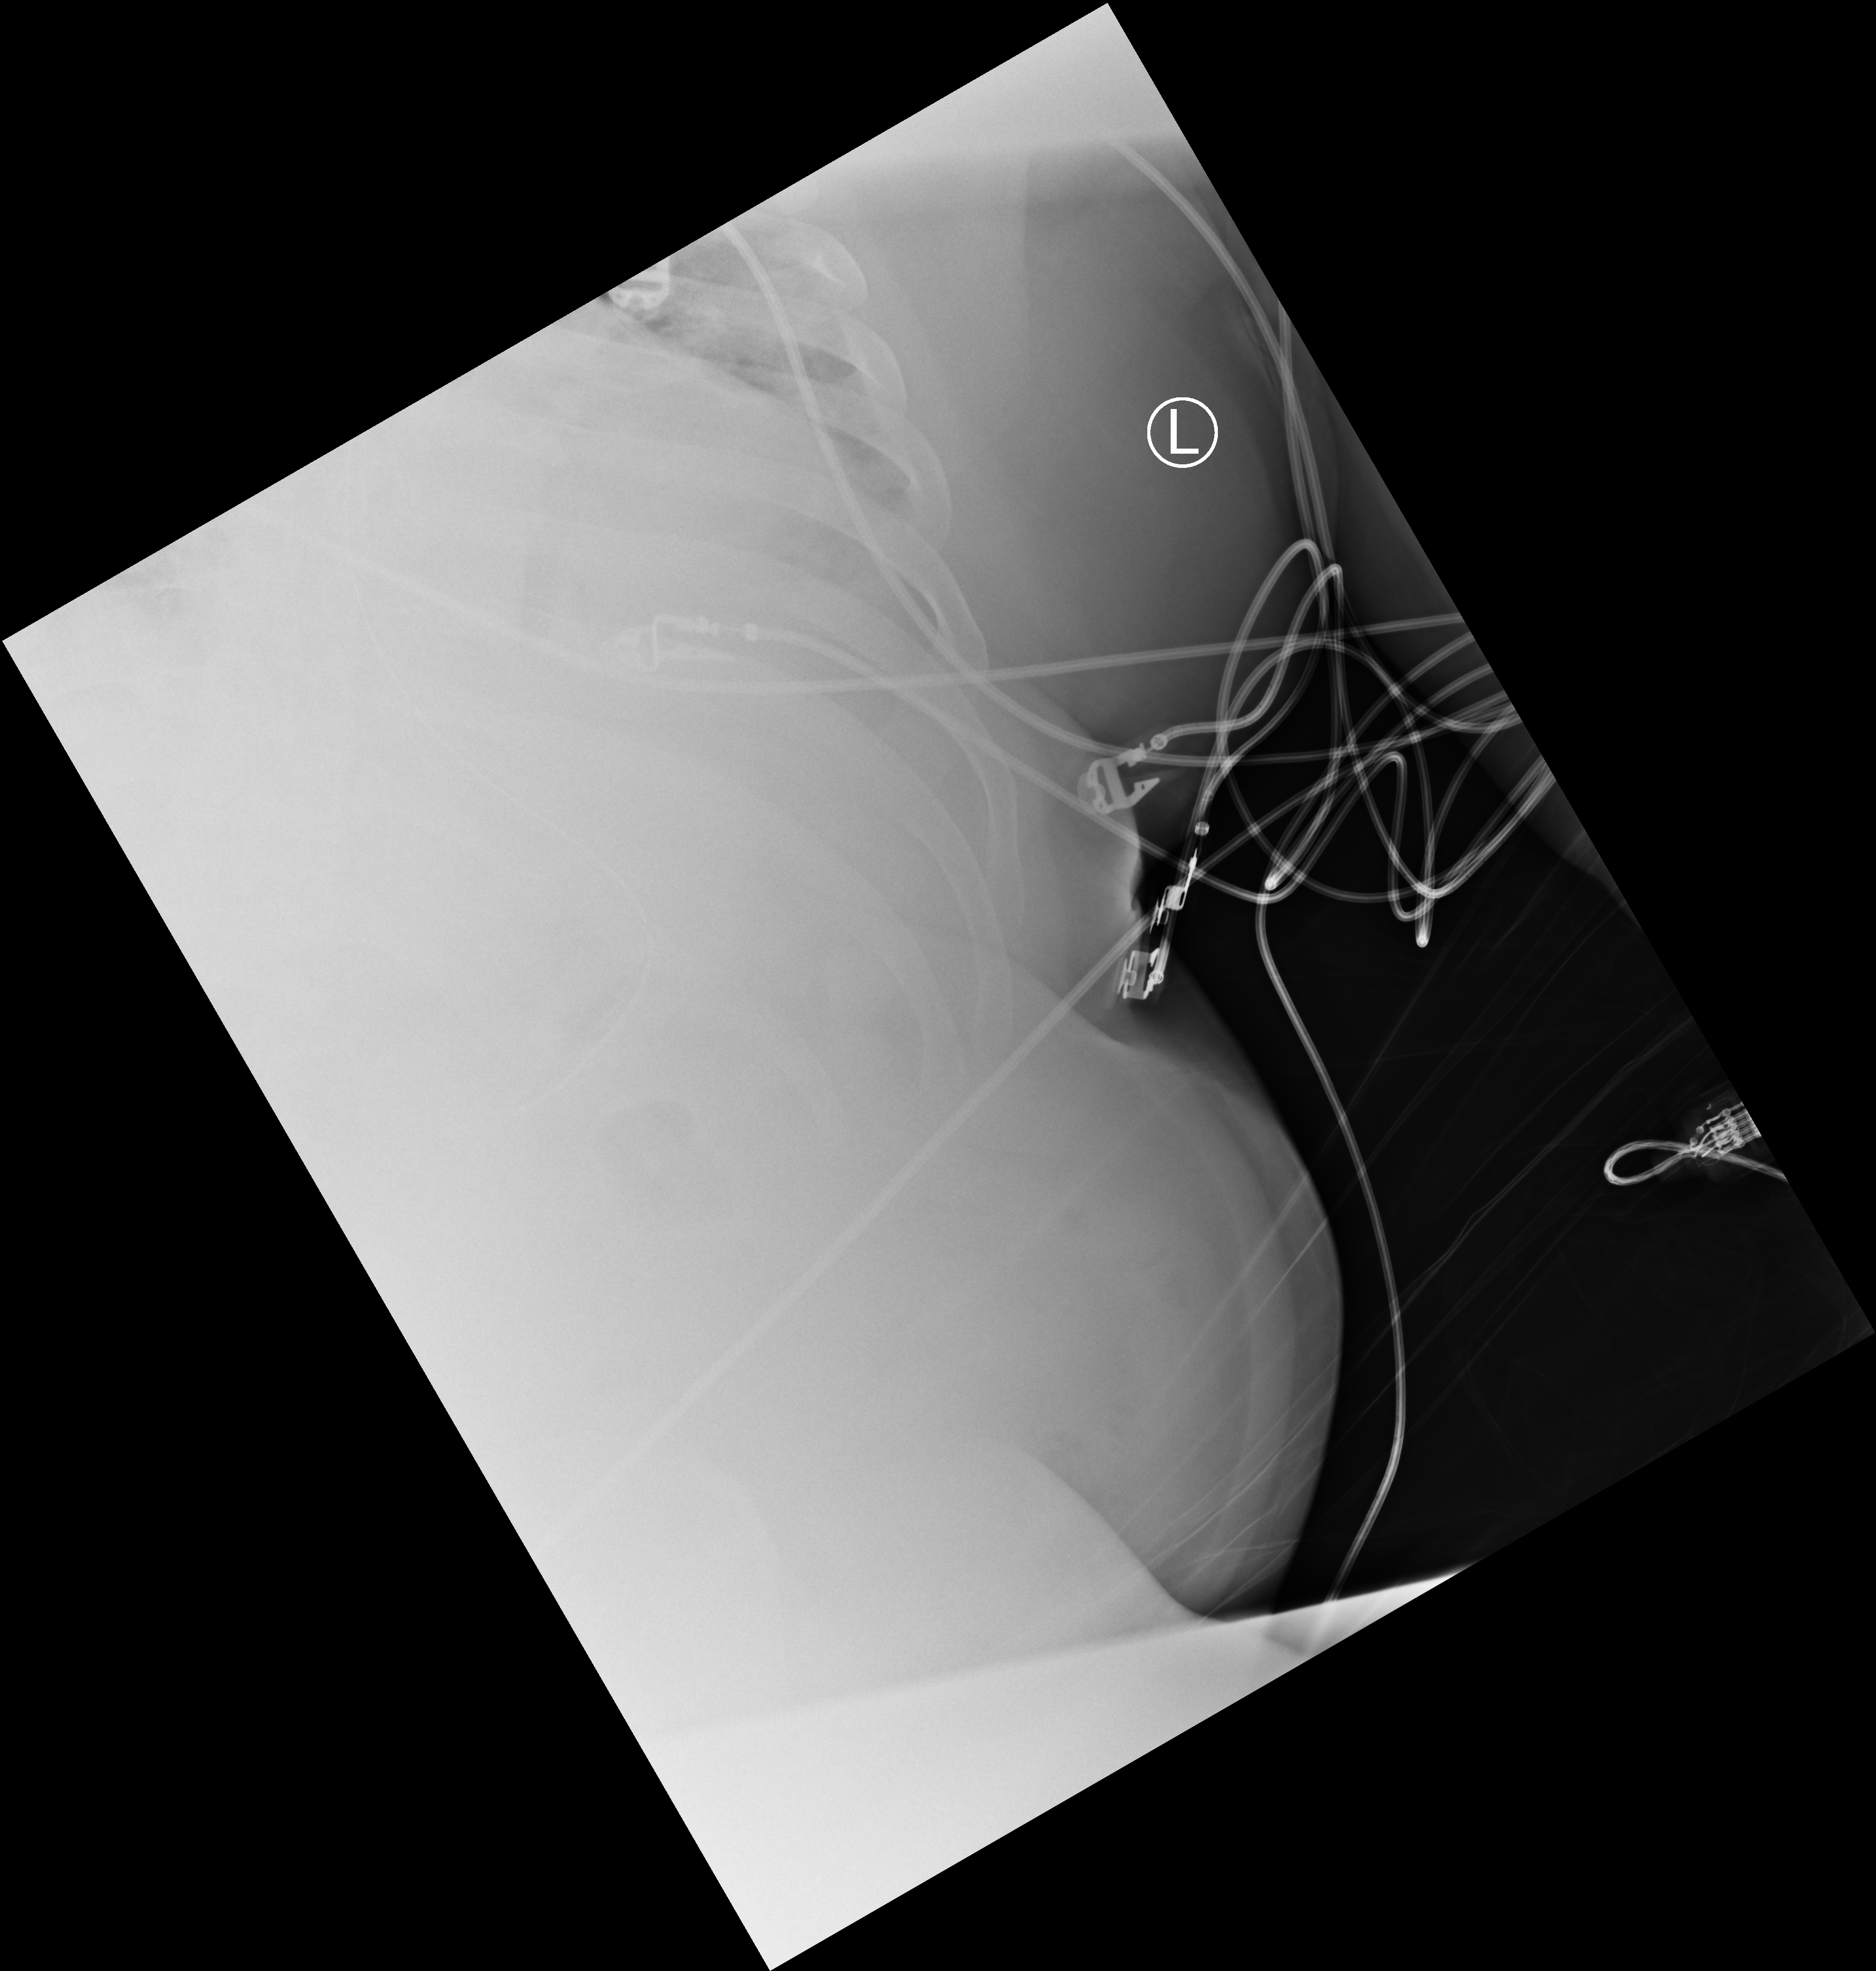
Chest X-ray (portable); anteroposterior (AP) projection. Patient hospitalised with COVID-19; male, aged 18–59 years.
Hospital-stay facts (about this admission, not read from this image; timing relative to this image not recorded): mechanically ventilated during this hospital stay: yes; admitted to intensive care during this hospital stay: yes; chronic kidney disease (admission record): yes.